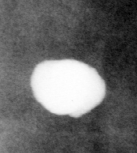
Crop from a digitized film mammogram around one marked abnormality; left breast; MLO view; BI-RADS breast density category 2 (scale 1–4).
Calcifications, morphology coarse; BI-RADS assessment category 2; subtlety rating 5 on a 1 (subtle) to 5 (obvious) scale; benign without callback (not worked up further).